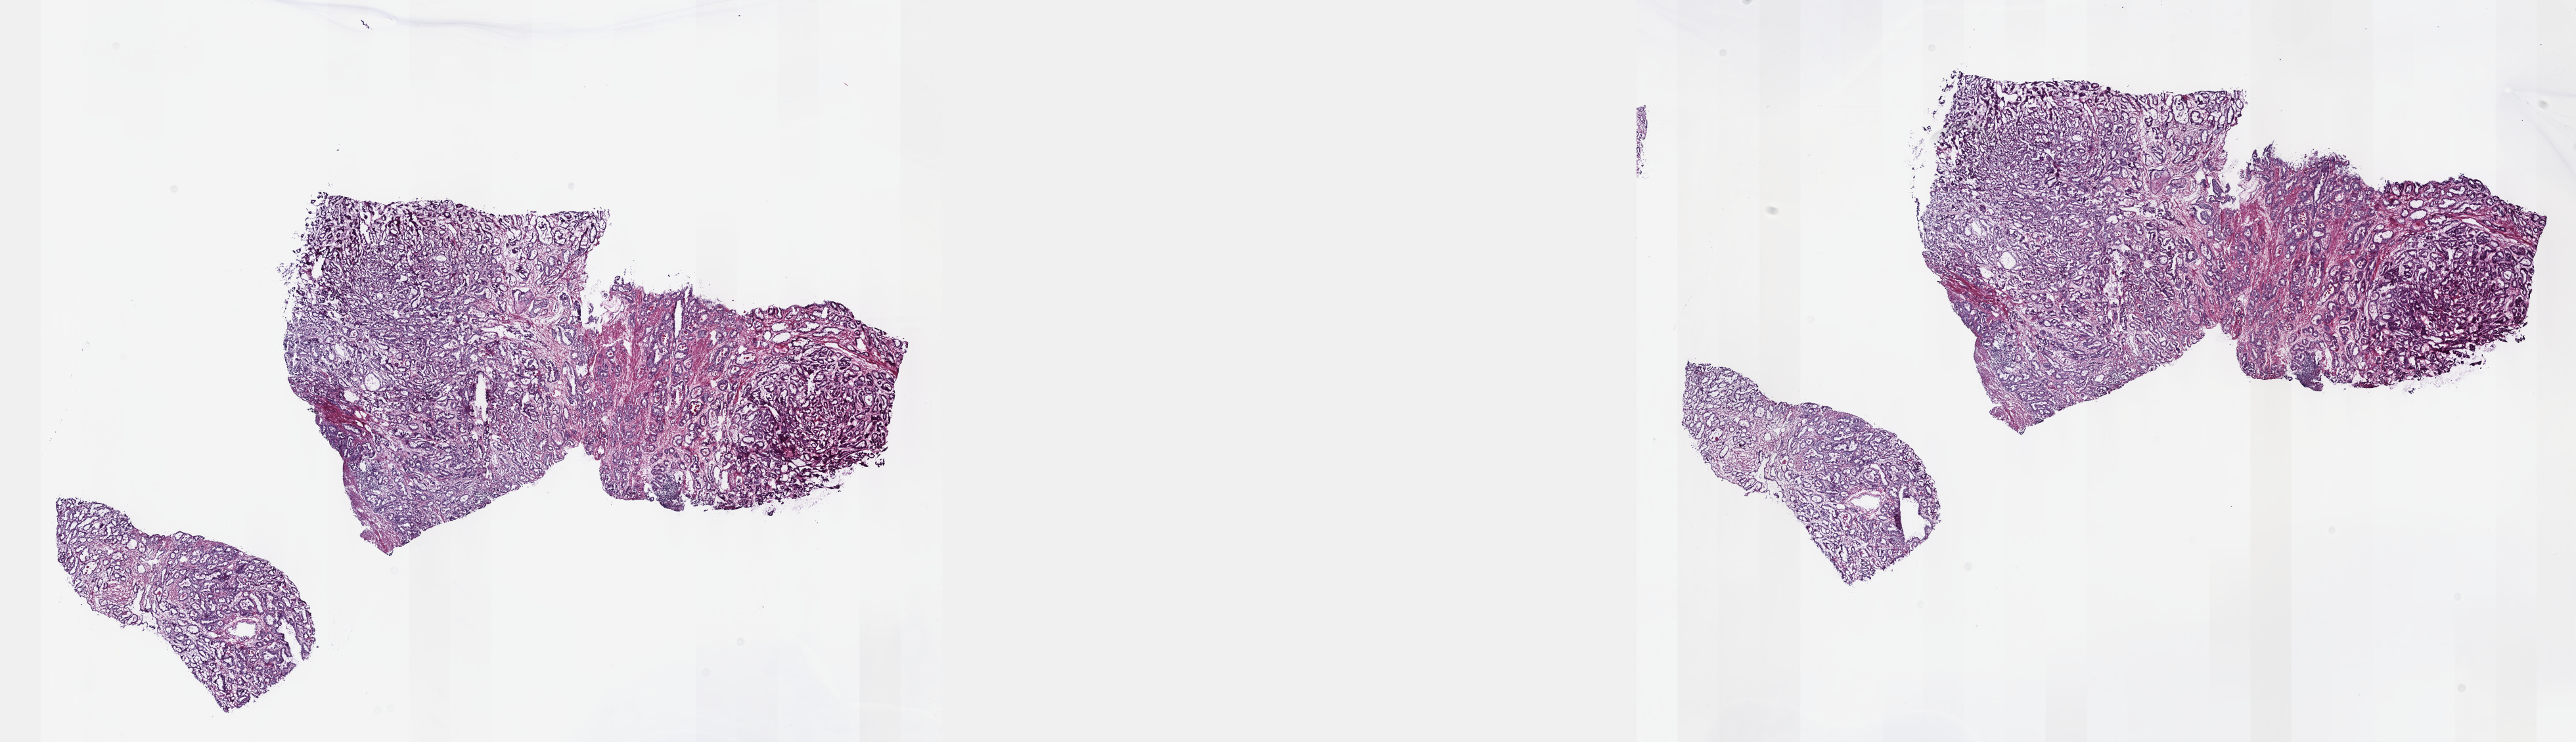
Digitized H&E tissue section (whole slide) — whole scanned area (about 31.7 x 9.1 mm) shown as a low-resolution overview. Frozen section from the top of the tissue portion. Prostate, primary tumour sample. Male, age 59 years at initial diagnosis. Gleason score: 6 (3+3). Slide review estimates, as recorded: tumour cells 75%, tumour nuclei 80%, normal cells 0%, stromal cells 25%, necrosis 0%. Inflammatory infiltration, as recorded: lymphocyte infiltration 0%, monocyte infiltration 0%, neutrophil infiltration 0%.
Histologic diagnosis: Adenocarcinoma, NOS. Lymph nodes positive (case pathology): 0 of 1 examined.